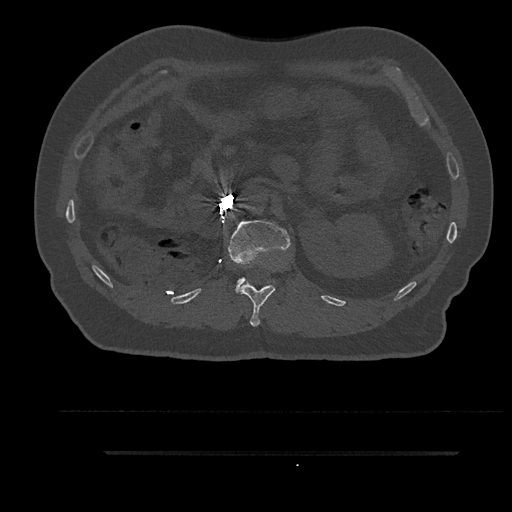
CT including the spine, one axial slice. Slice 209 of 797 in the series (ordered by position). 120 kVp. Bone window (W 1800 / L 400 HU). 0.5 mm slice thickness. 512 × 512 image matrix. Male patient, age 63 years. Case-level facts recorded for this patient, not image findings: primary cancer: renal; vertebrae with lytic lesions (as recorded): T8.
Outlined on this slice (semi-automatic segmentation, software-assisted and operator-edited):
- L1 vertebra: bounding box [x1, y1, x2, y2] px = [228, 220, 290, 293]
- T12 vertebra: [239, 282, 275, 326]